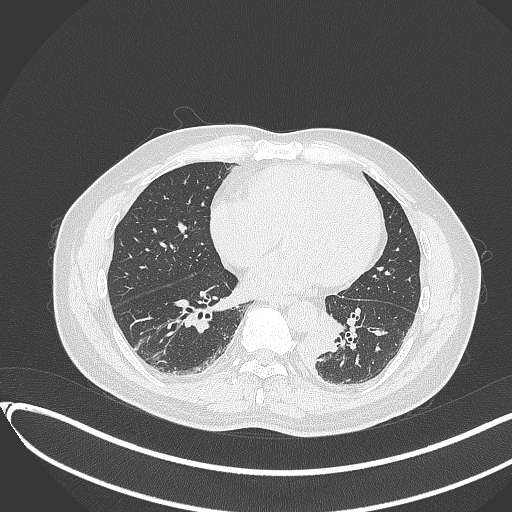
Chest CT, one axial slice; position 126 of 417 along the scan axis; reconstruction kernel B70f; 120 kVp; lung window (W 1500 / L -600 HU); 1 mm slice thickness; 512 × 512 image matrix, field of view 400 × 400 mm. Male patient, age 54 years. Case-level facts recorded for this patient, not image findings: clinical TNM (as recorded): T3 N0 M0.
Outlined on this slice (rectangle marked by the reading radiologist):
- lung tumour (recorded histology: squamous cell carcinoma): bounding box [x1, y1, x2, y2] px = [301, 313, 350, 369]